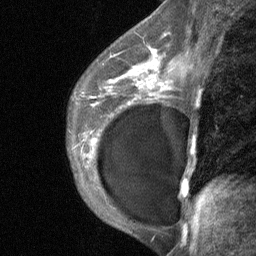
Breast MRI (dynamic contrast-enhanced), one sagittal slice. Slice 43 of 64 in the series (ordered by position). Dynamic contrast-enhanced study with each time point stored as its own series, time point 2 of 3 at this slice position (early post-contrast, ordered by acquisition time). 1.5 T. TE 4.8 ms, TR 27 ms. 2 mm slice thickness. 256 × 256 image matrix, field of view 180 × 180 mm. Female patient, age 35 years. From the clinical record (not read from this slice): setting: breast cancer imaged before/during neoadjuvant chemotherapy; receptor status: HR-positive, HER2-negative.
Outlined on this slice (semi-automatically segmented with operator editing):
- analysis volume of interest (the breast-tissue region the enhancement analysis was run in; not a lesion): bounding box <74,58,176,171> (left, top, right, bottom; pixels)
- tumour enhancement mask (voxels above the 90 % enhancement threshold inside the analysis volume of interest): <137,61,162,86>